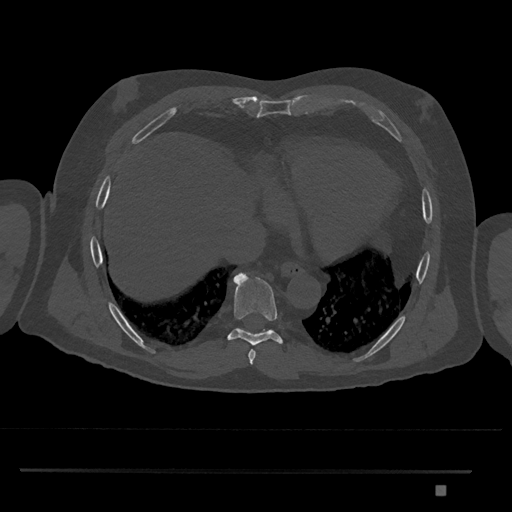
CT including the spine, one axial slice; position 1107 of 1134 along the scan axis; reconstruction kernel Br40s/3; bone window (W 1800 / L 400 HU); 512 × 512 image matrix. Male patient, age 65 years. From the clinical record (not read from this slice): primary cancer: prostate.
Annotated regions visible in this slice (semi-automatic segmentation, software-assisted and operator-edited):
- T8 vertebra: box from (x=227, y=272) to (x=283, y=346) px